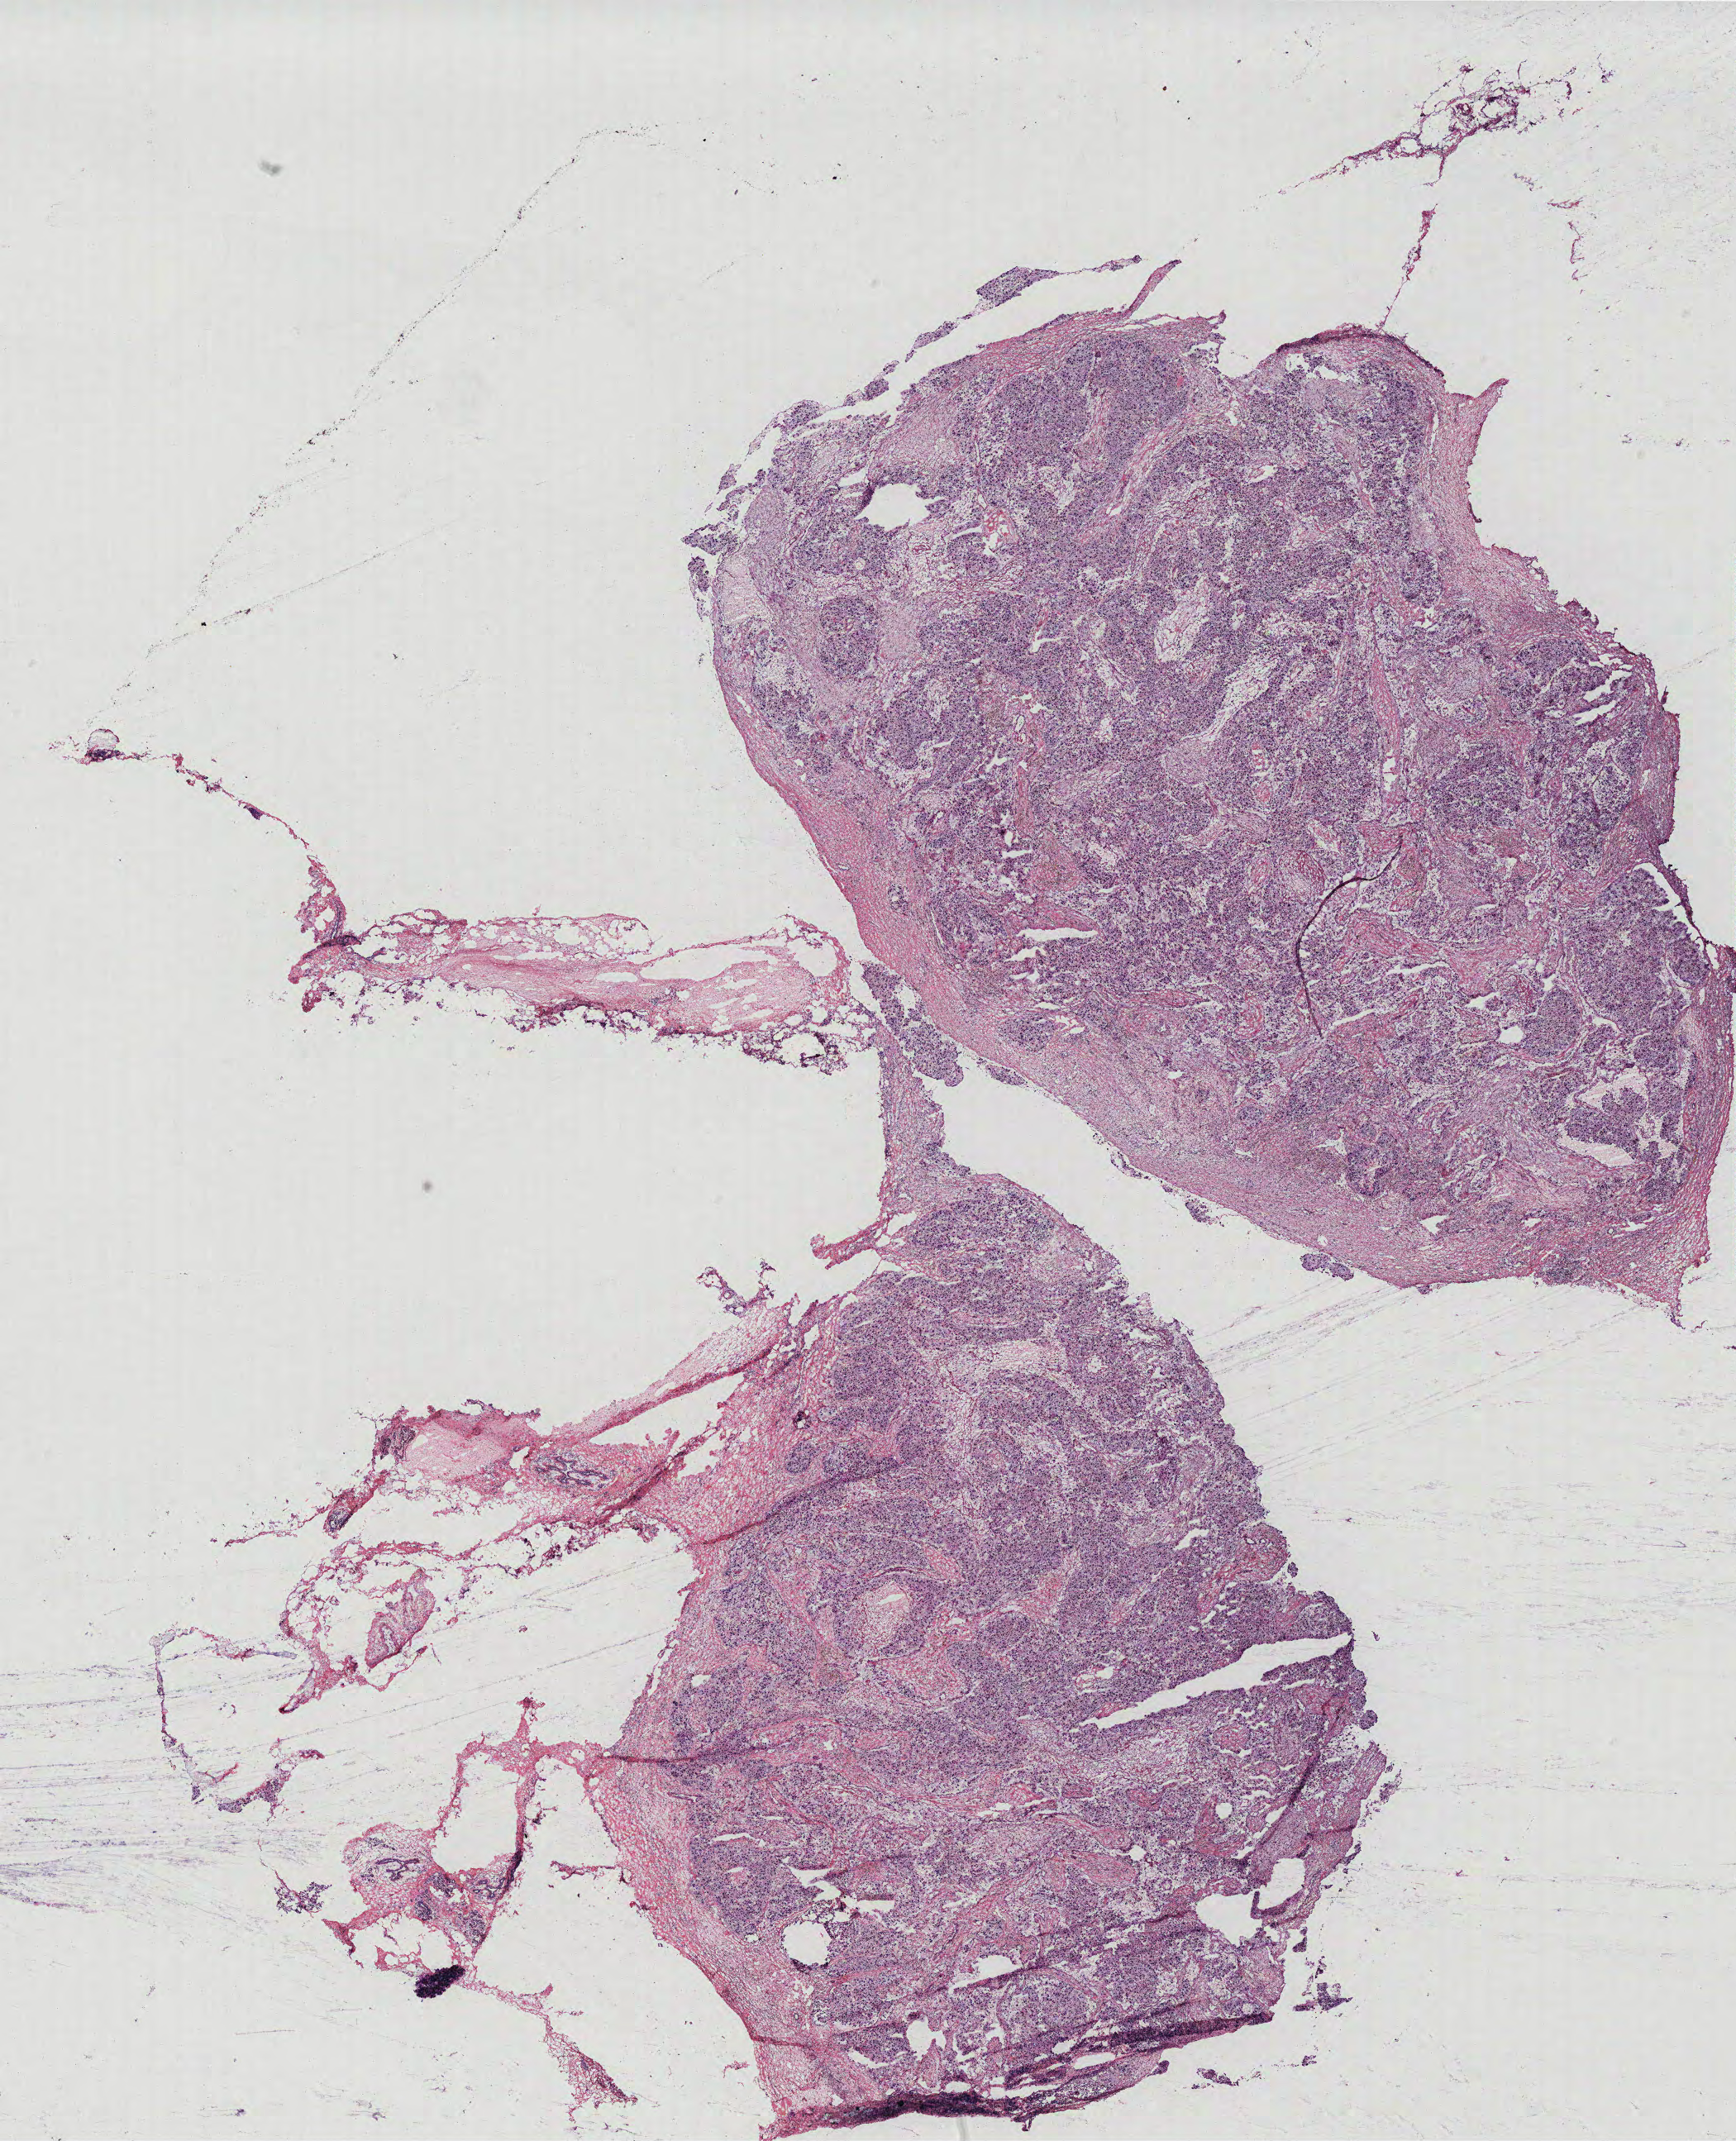
Whole-slide histology image, Hematoxylin and eosin (H&E) stained — shown as a low-resolution overview of the whole scanned area (about 16.8 x 20.7 mm, acquisition: 40x scan), breast, tissue type not recorded.
• patient diagnosis (cohort enrolment): breast cancer (breast)